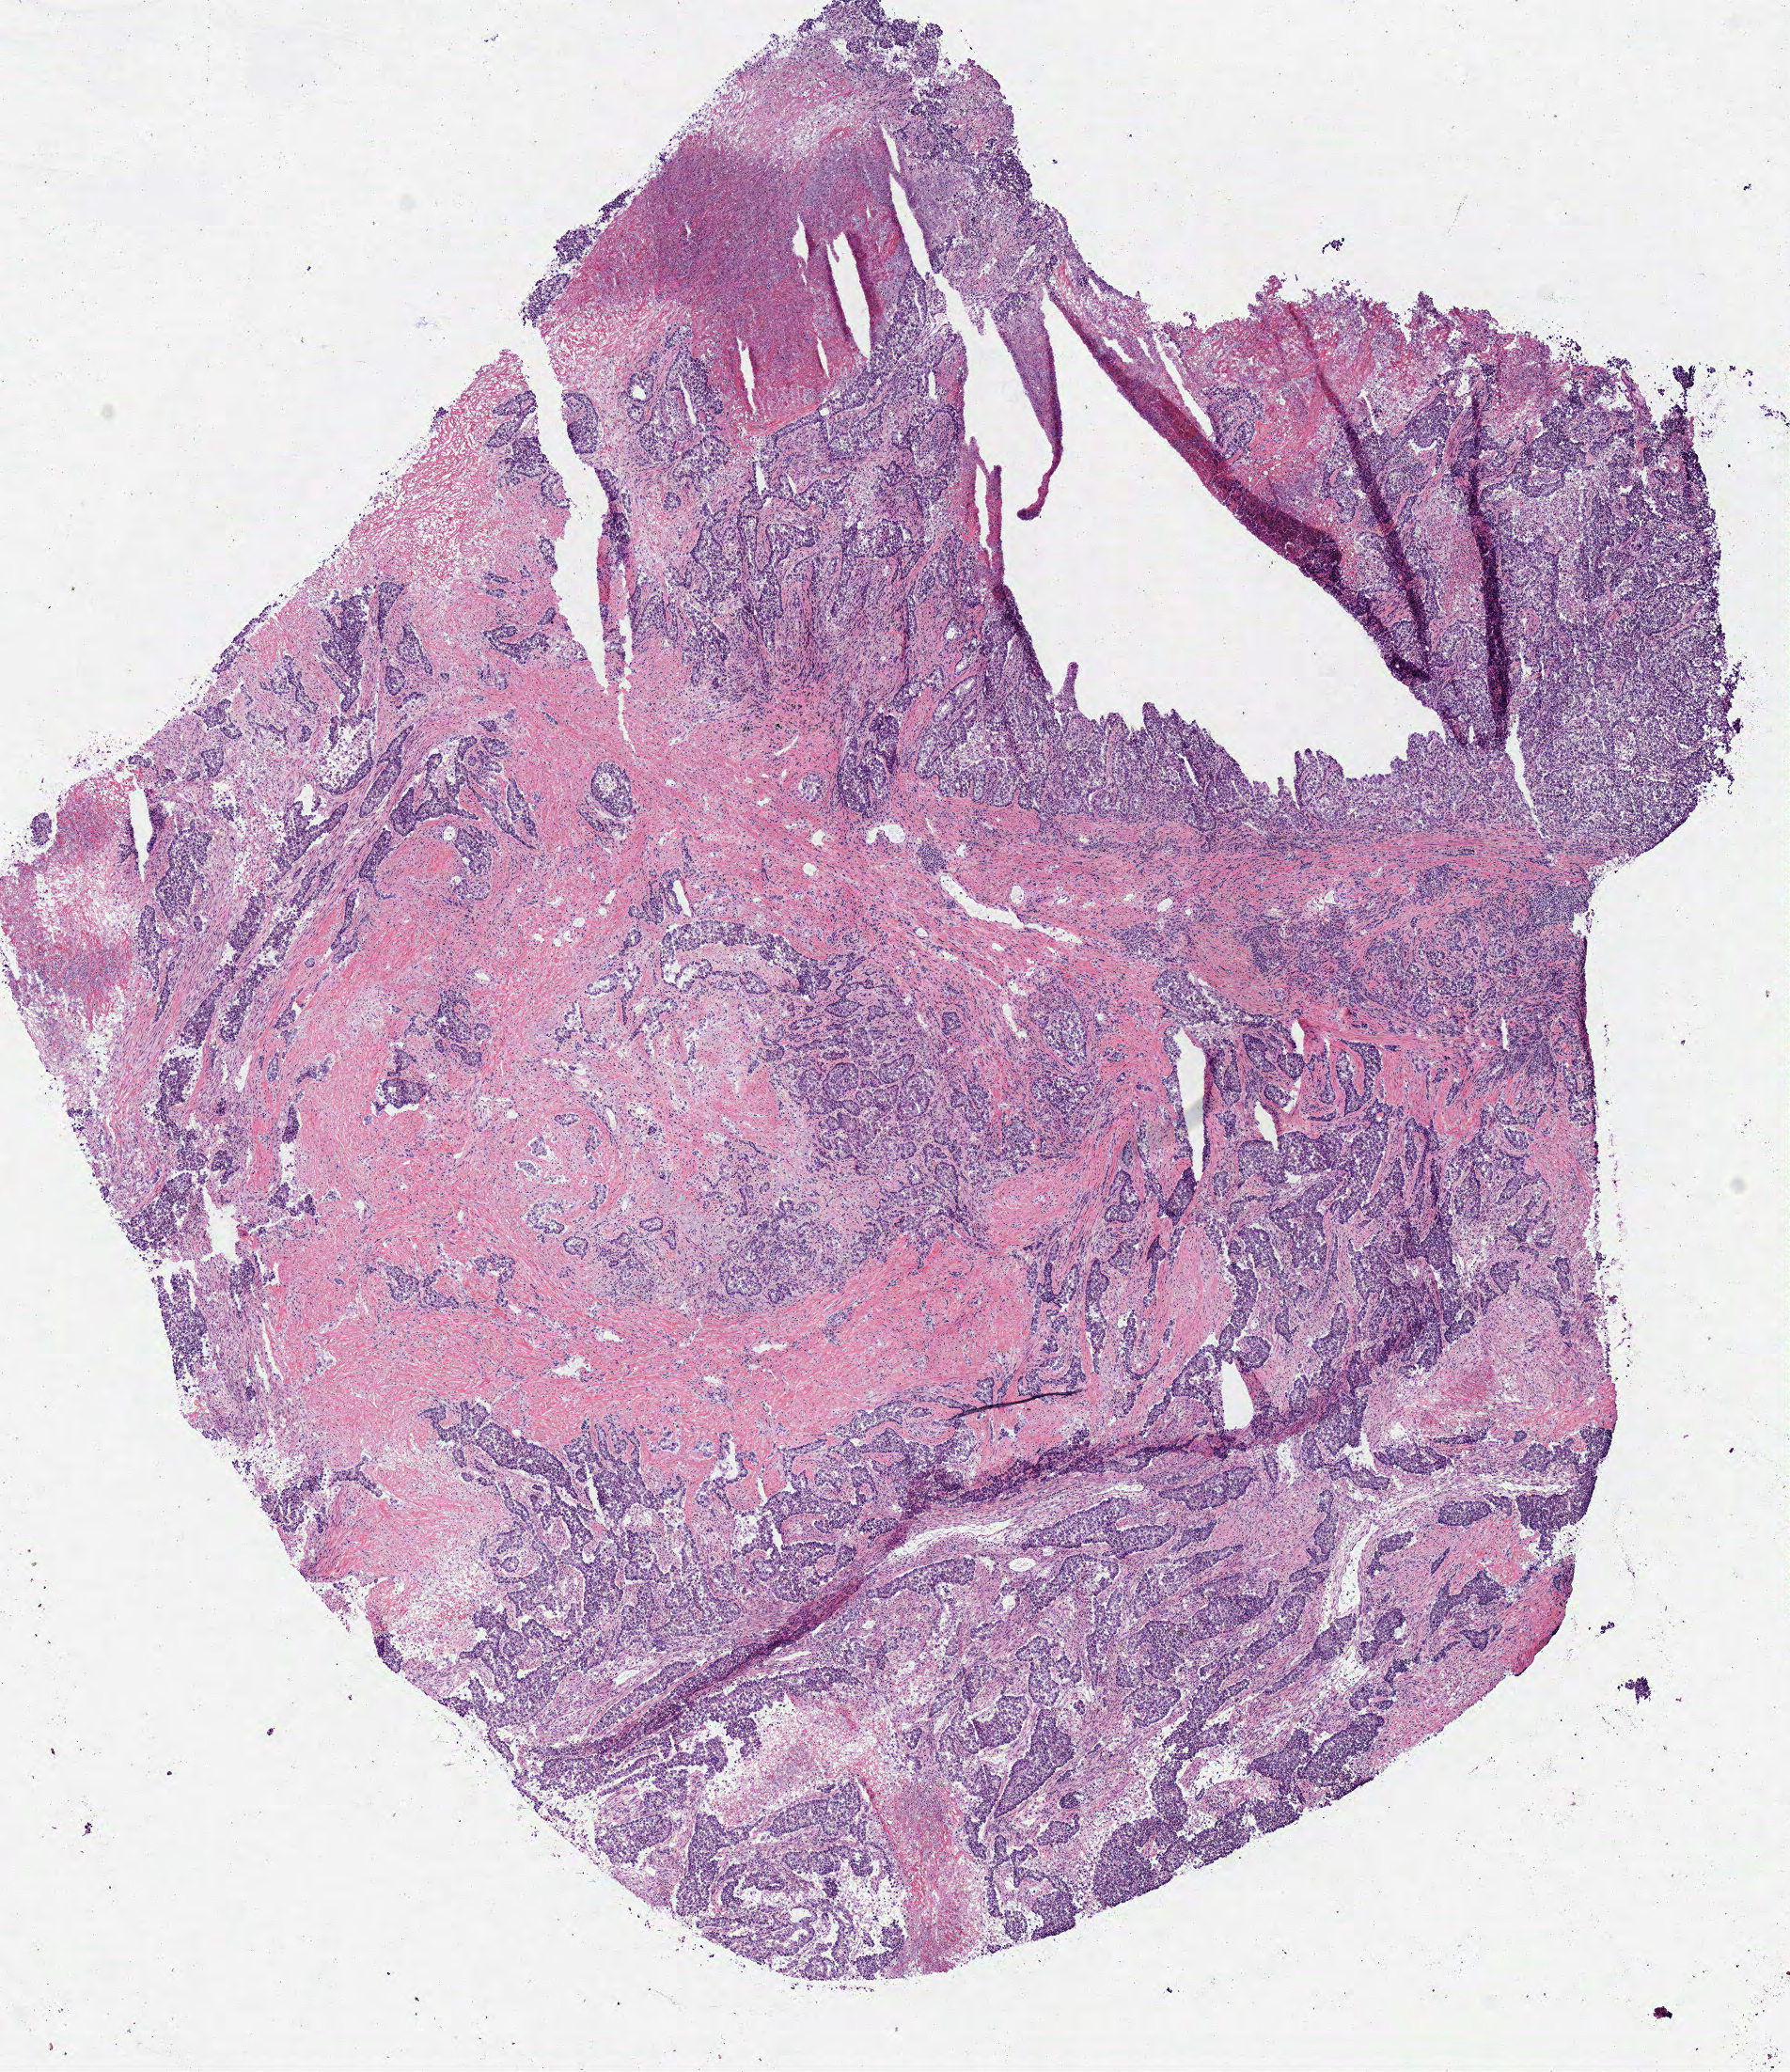
H&E-stained whole-slide image — shown as a low-resolution overview of the whole scanned area (about 7.5 x 8.7 mm), frozen section from the bottom of the tissue portion, lung, primary tumour sample. Male, age 66 years at initial diagnosis. Pathologist review of this section (percent, as recorded): tumour cells 65%, tumour nuclei 80%, normal cells 0%, stromal cells 25%, necrosis 10%.
Diagnosis: Adenocarcinoma, NOS (middle lobe, lung). AJCC pathologic stage: IB (5th edition).